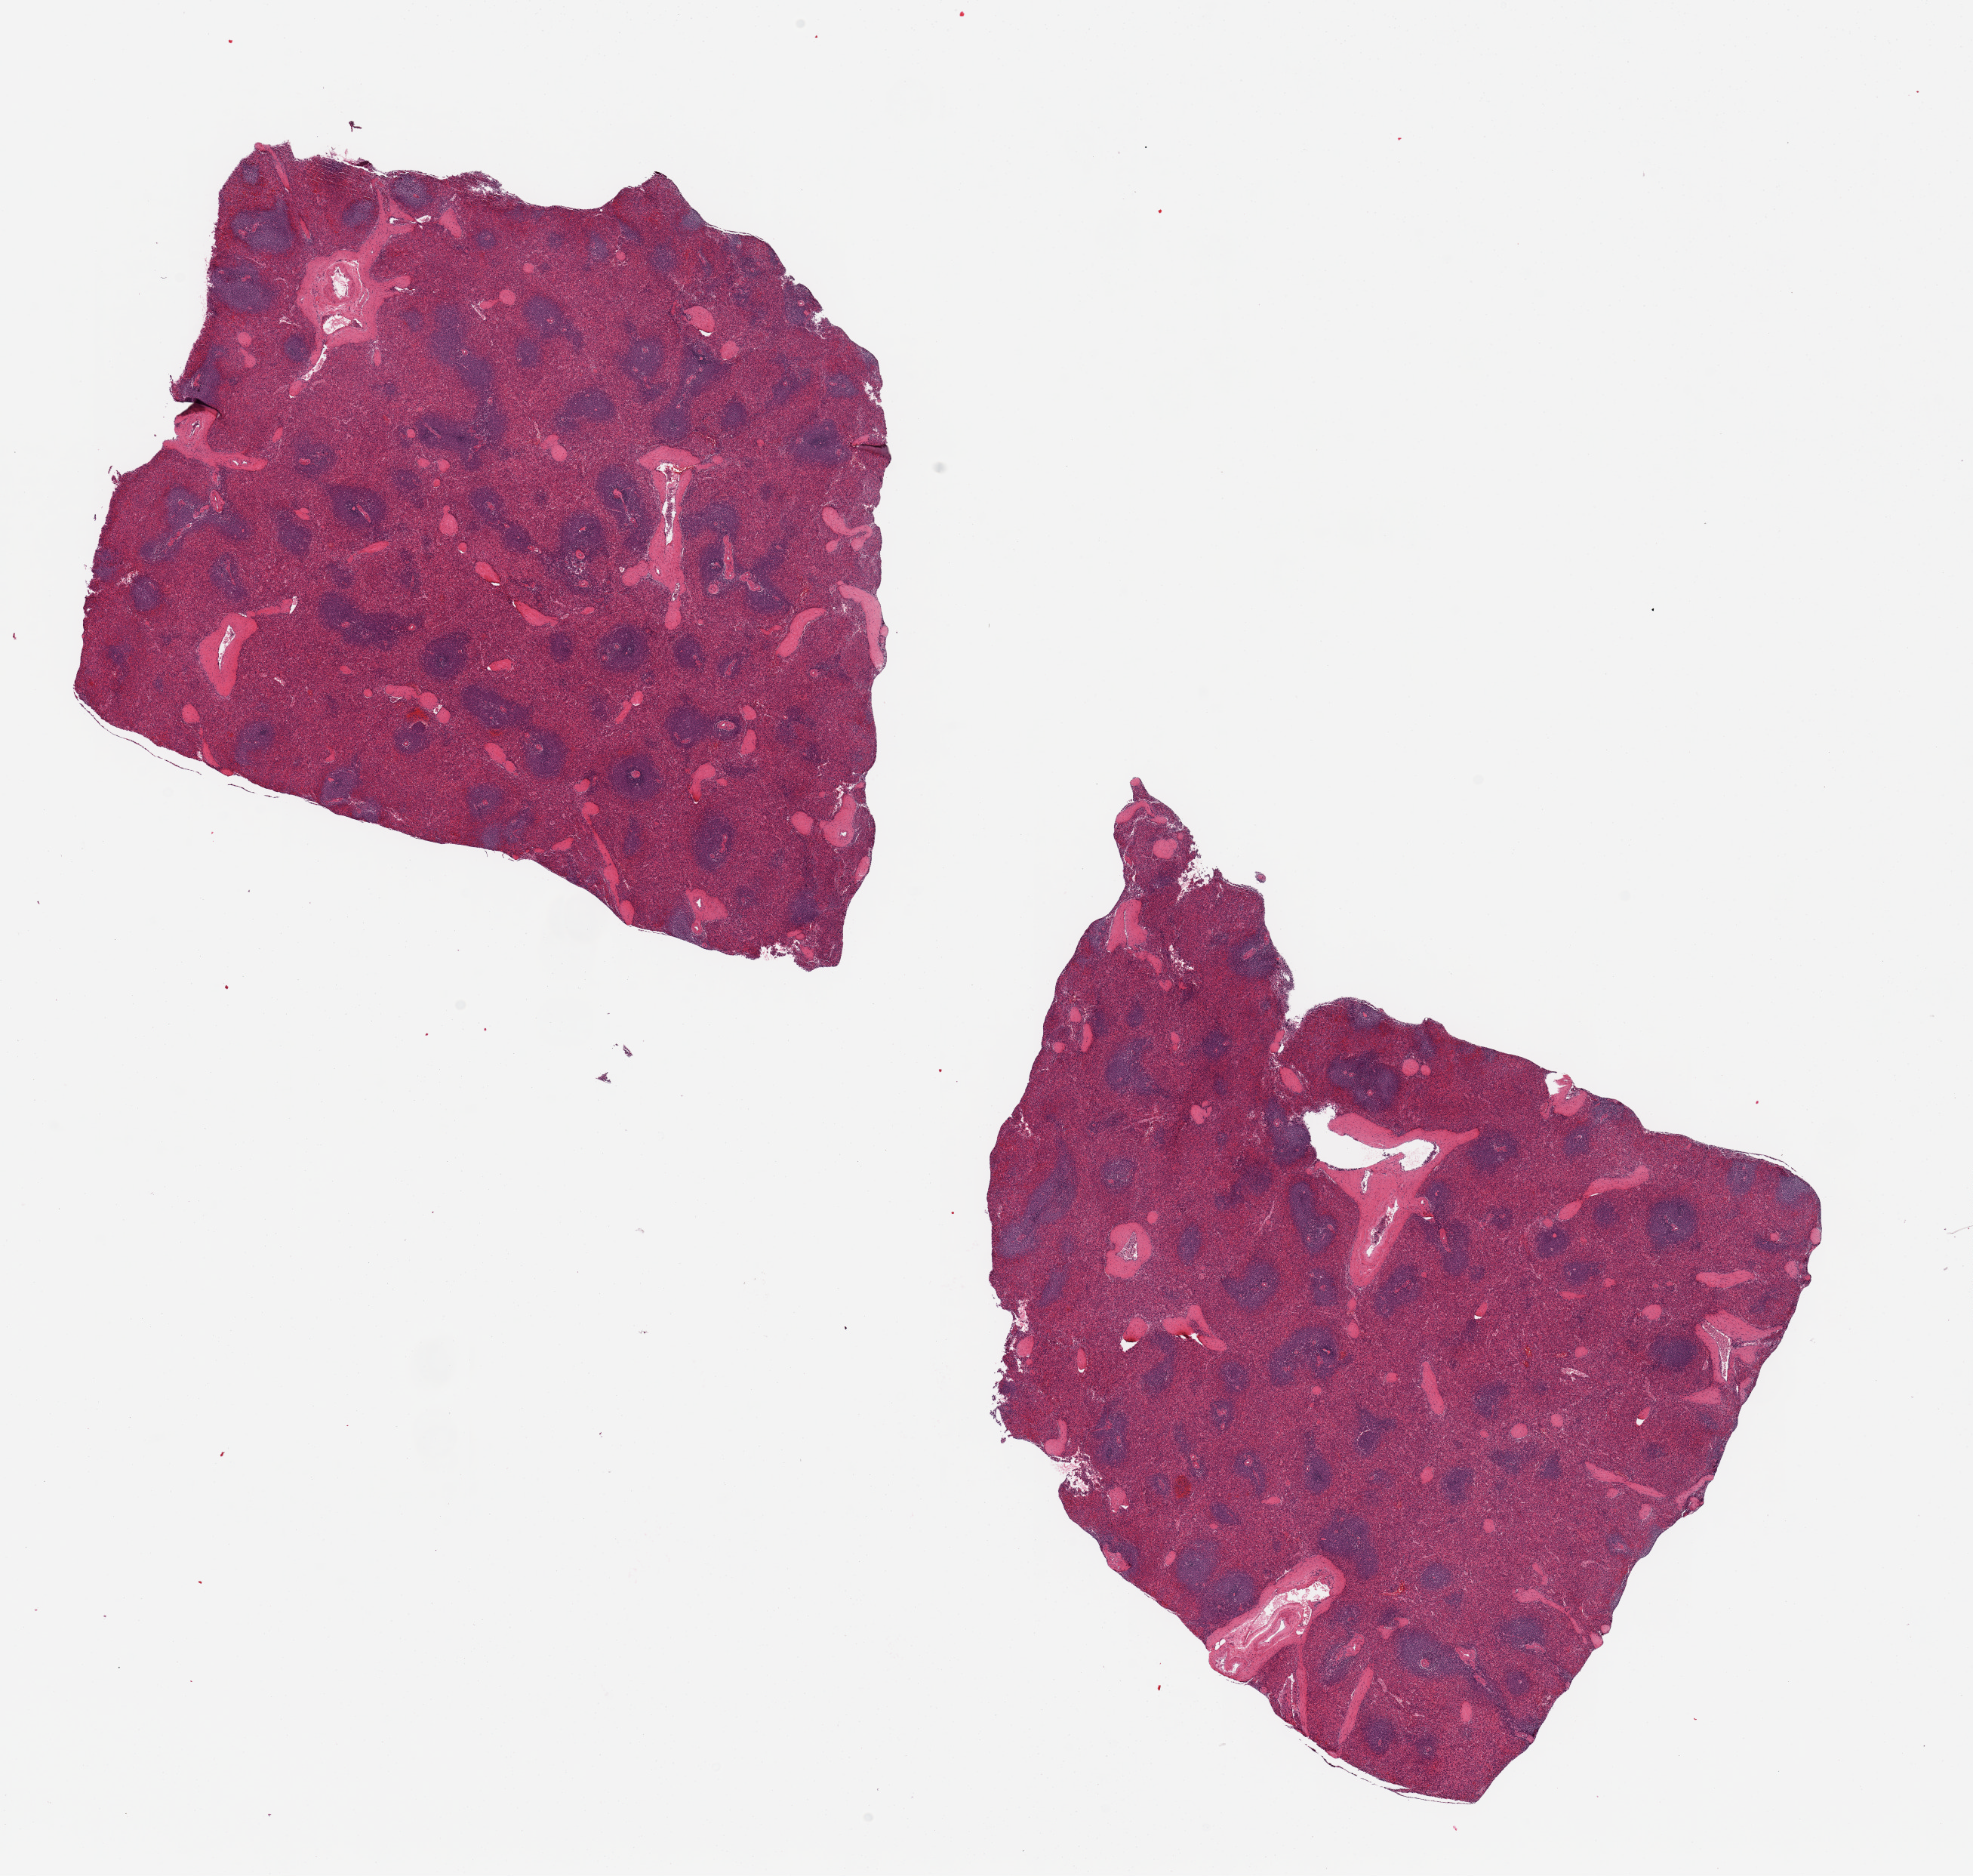
H&E whole-slide image — low-resolution overview of the scanned area, about 20.7 x 19.7 mm; PAXgene-fixed, paraffin-embedded tissue; sampled site (target tissue): spleen; tissue donor sample.
Reviewer comment on this tissue sample: 2 pieces.